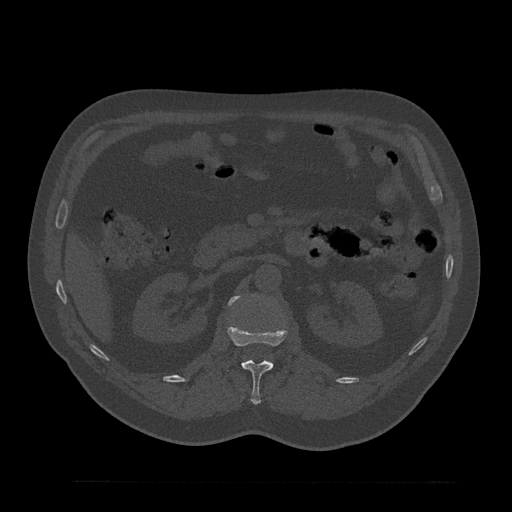
CT including the spine, one axial slice; slice 149 of 797 in the series (ordered by position); bone window (W 1800 / L 400 HU); 0.5 mm slice thickness; 512 × 512 image matrix, field of view 430 × 430 mm. Male patient, age 61 years. From the clinical record (not read from this slice): primary cancer: prostate.
Outlined on this slice (semi-automatically segmented with operator editing):
- L1 vertebra: box from (x=227, y=323) to (x=287, y=405) px
- L2 vertebra: (x=228, y=296)–(x=239, y=305)